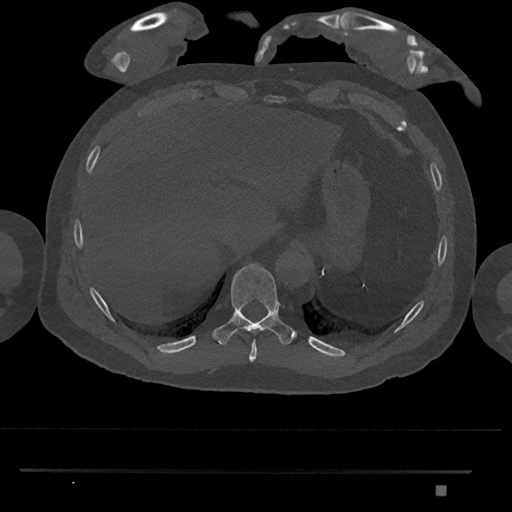
CT including the spine, one axial slice; slice 1007 of 1134 in the series (ordered by position); reconstruction kernel Br40s/3; 120 kVp; bone window (W 1800 / L 400 HU); 0.5 mm slice thickness; 512 × 512 image matrix, field of view 429 × 429 mm. Male patient, age 65 years. From the clinical record (not read from this slice): primary cancer: prostate.
Outlined on this slice (semi-automatic segmentation, software-assisted and operator-edited):
- T10 vertebra: bounding box (x1, y1, x2, y2) in pixels: (212, 263, 296, 345)
- T9 vertebra: (249, 340, 257, 362)